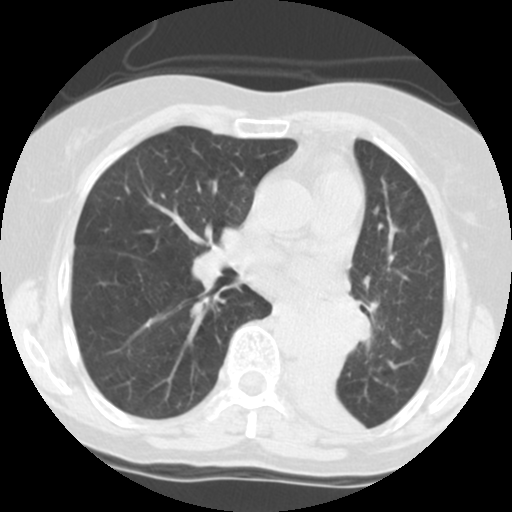
Axial slice from a low-dose chest CT screening exam, third annual screen, lung window (W 1500 / L -600 HU), standard (soft-tissue) reconstruction kernel (STANDARD), 140 kVp. Female participant, aged 56 years at enrolment.
Lesion marked by an expert reader, bounding box [x1, y1, x2, y2] px = [308, 299, 369, 354]. Screening reader's record for this exam: no non-calcified nodule ≥4 mm recorded. Official screen result: positive, other. Later outcome: lung cancer diagnosed 9 days after this screen — squamous cell carcinoma, NOS, left main stem bronchus, poorly differentiated (G3), stage IIIA (AJCC 6th edition).